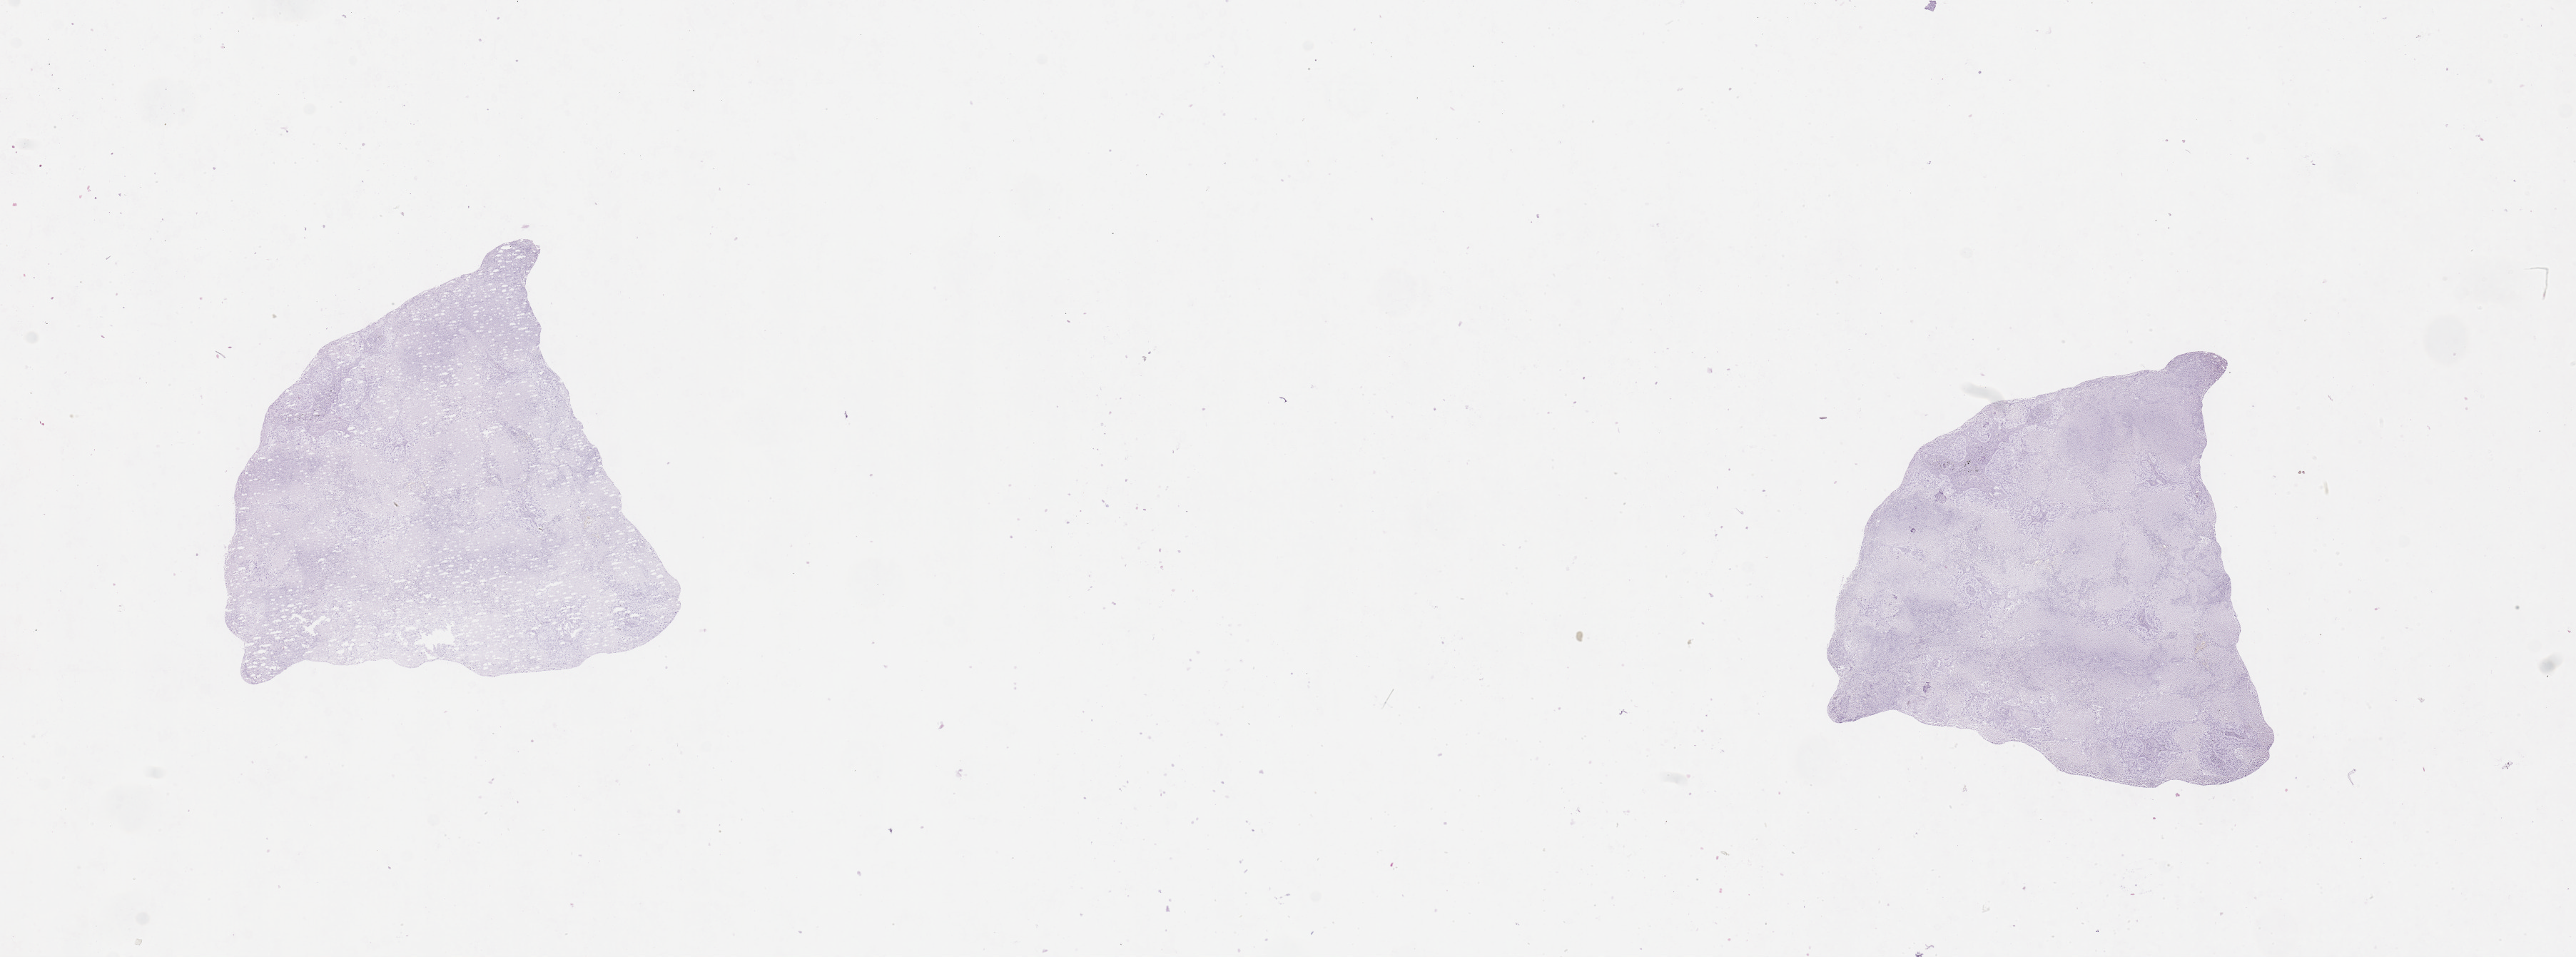
Digitized H&E tissue section (whole slide) — low-resolution overview of the scanned area, about 28.5 x 10.6 mm; tumour tissue sample, lung. 74-year-old male patient. Histologic grade: G2 (moderately differentiated).
- AJCC pathologic stage: IIIA
- diagnosis: Squamous cell carcinoma, NOS
- primary tumour site (as recorded): left lower lobe